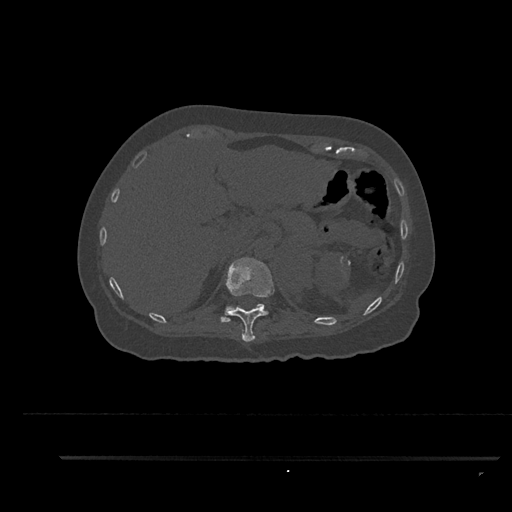
CT including the spine, one axial slice. Slice 302 of 797 in the series (ordered by position). Reconstruction kernel Br40s/3. 120 kVp. Bone window (W 1800 / L 400 HU). 0.5 mm slice thickness. 512 × 512 image matrix, field of view 408 × 408 mm. Female patient, age 44 years. Case-level facts recorded for this patient, not image findings: primary cancer: renal.
Structures marked on this image (semi-automatically segmented with operator editing):
- T11 vertebra: box from (x=225, y=257) to (x=275, y=343) px
- T12 vertebra: (x=220, y=304)–(x=265, y=323)